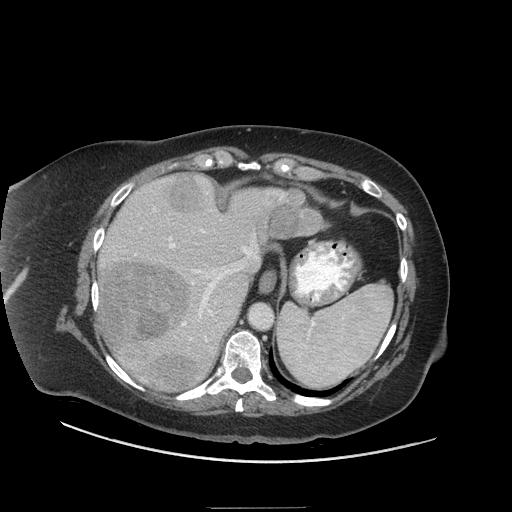
Contrast-enhanced abdominal CT (liver protocol), one axial slice. Position 49 of 81 along the scan axis. Reconstruction kernel STANDARD. Soft-tissue window (W 400 / L 40 HU). 2.5 mm slice thickness. 512 × 512 image matrix. From the clinical record (not read from this slice): diagnosis: hepatocellular carcinoma (patient treated with transarterial chemoembolisation; whether this scan precedes or follows treatment is not stated here); TNM stage (as recorded): Stage-II; Child-Pugh class: A; tumour differentiation: moderately differentiated.
Outlined on this slice (semi-automatic segmentation, software-assisted and operator-edited):
- liver parenchyma outside the tumour (the mass and vessels are separate outlines, so this box may not span the whole liver): bounding box <96,174,288,392> (left, top, right, bottom; pixels)
- mass: <97,174,330,392>
- liver vessels: <113,180,283,380>